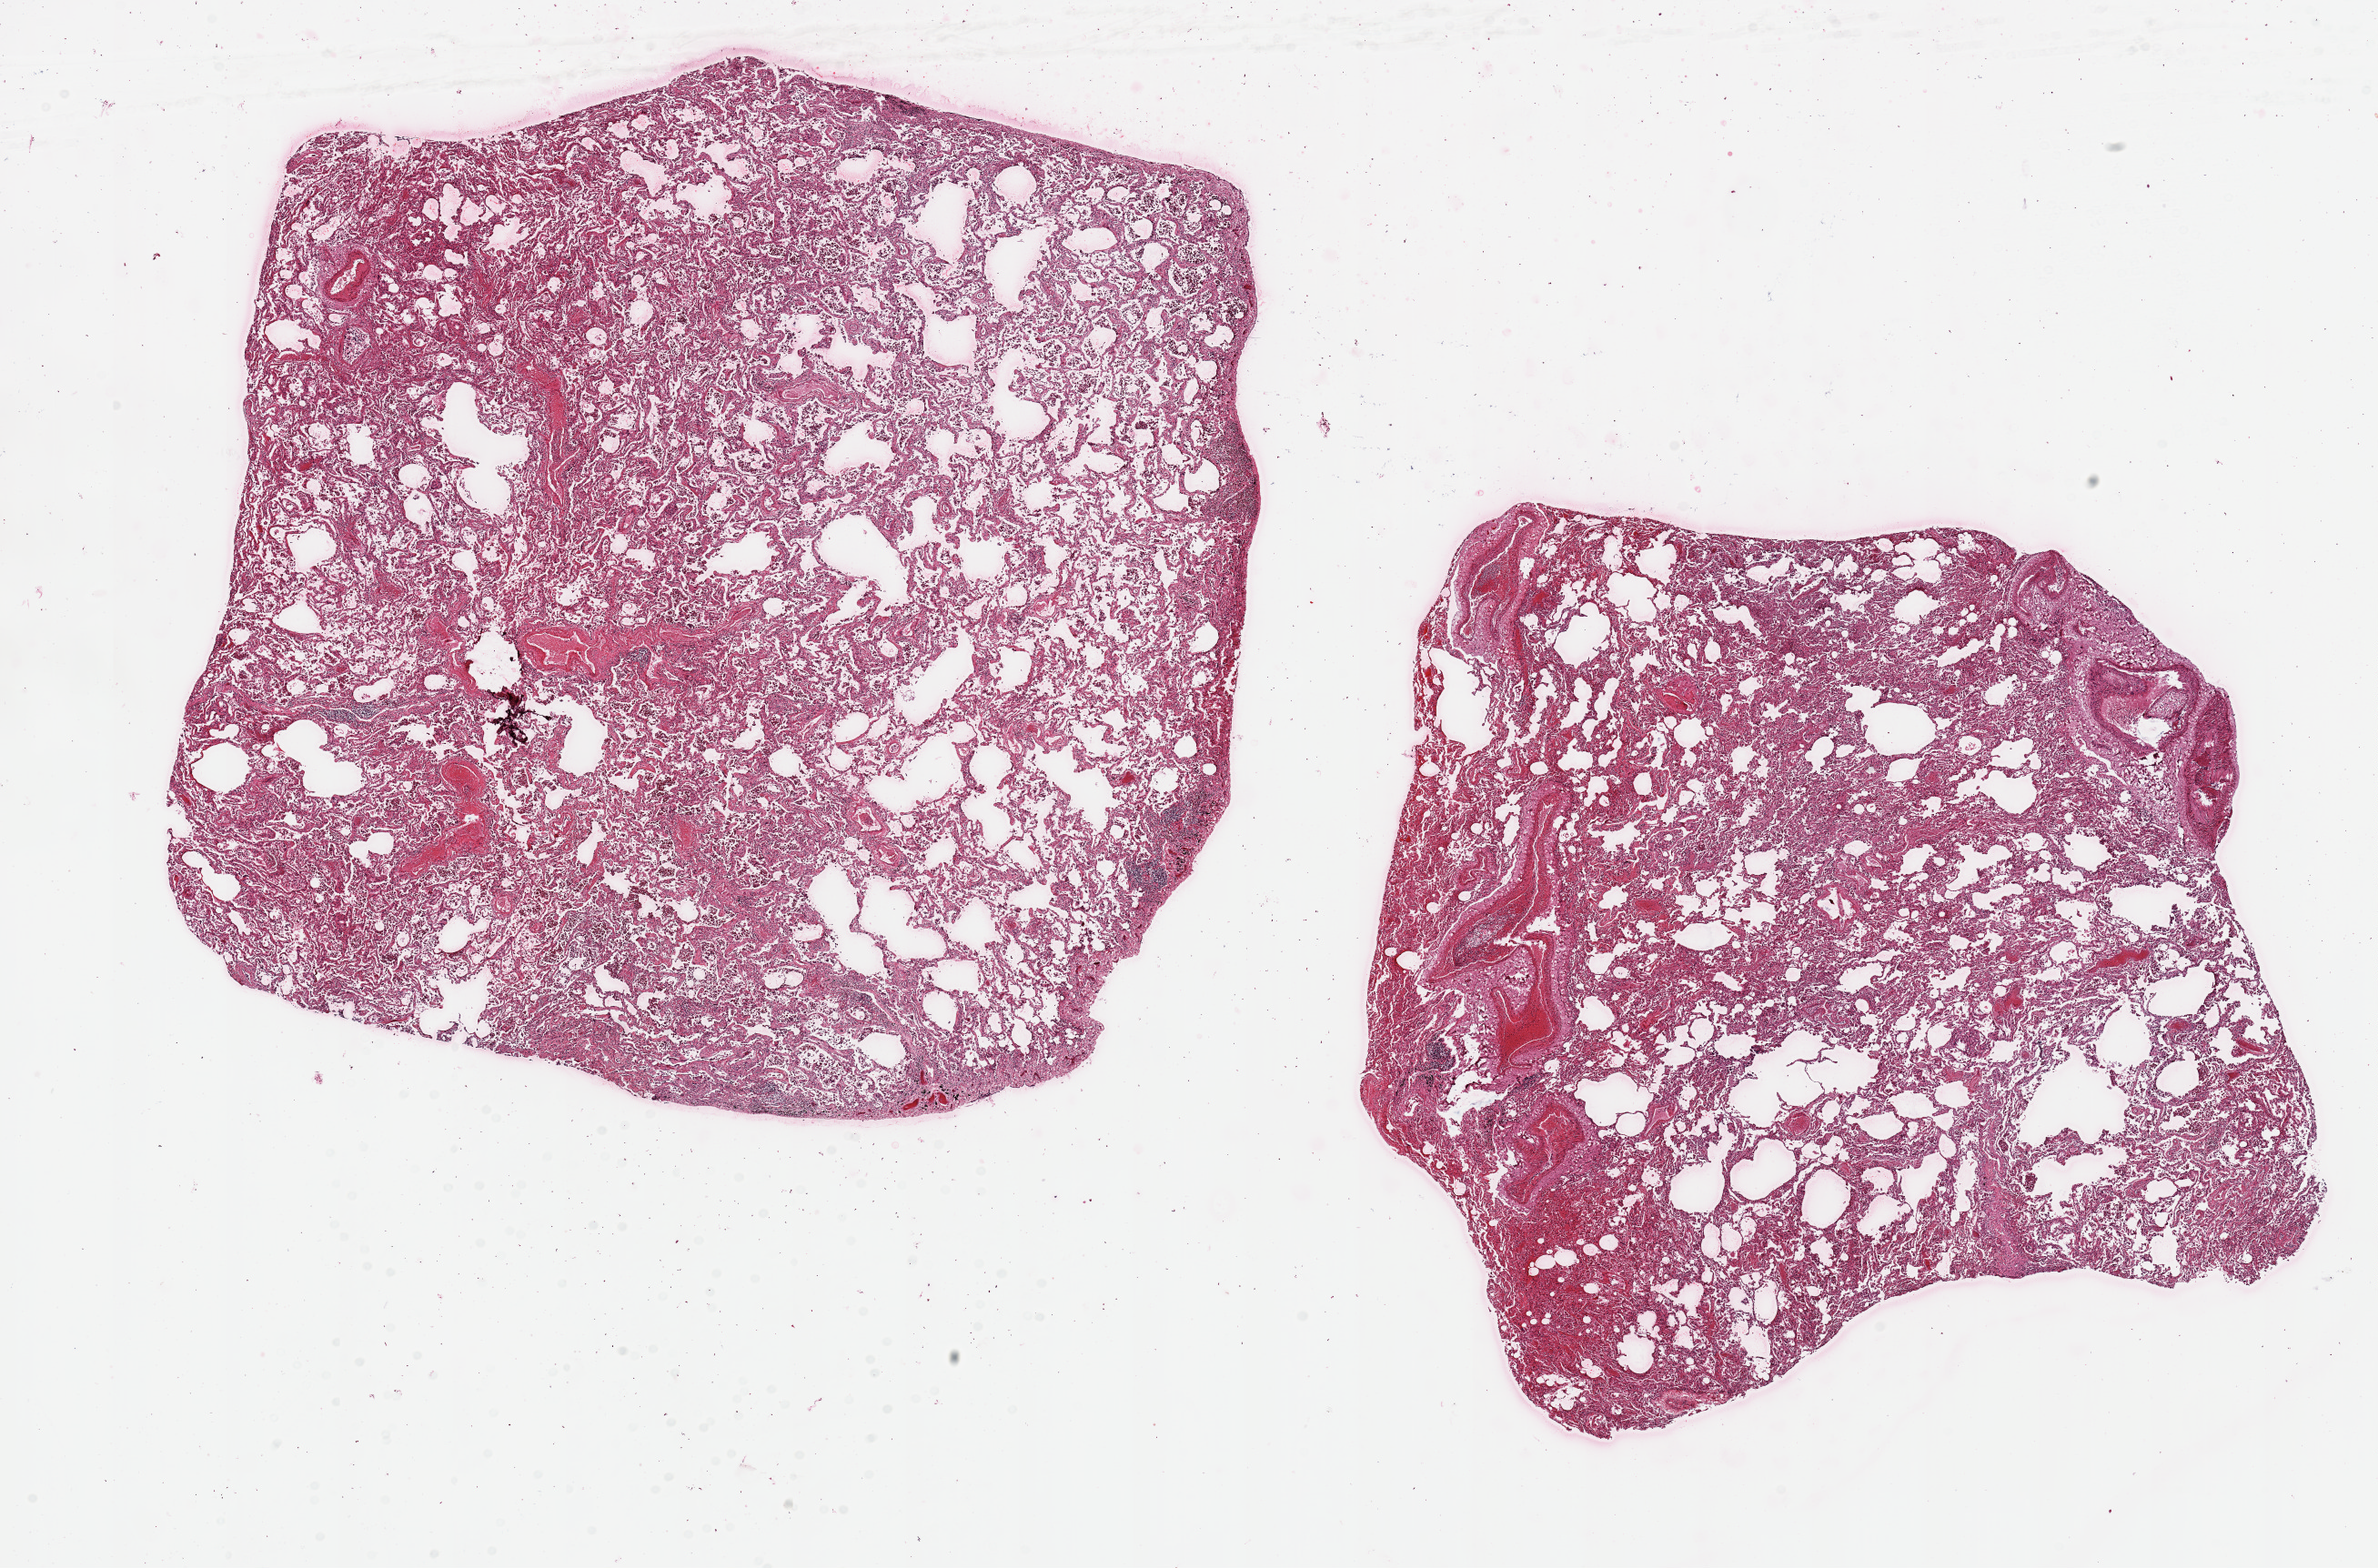
Digitized hematoxylin and eosin (H&E)-stained section, brightfield, low-resolution overview of the scanned area, about 20.7 x 13.6 mm; PAXgene-fixed paraffin-embedded (PFPE) section; target tissue: lung; donor tissue sample. Donor: male.
Review note (as recorded): 2 pieces, 9x9 & 8x8 mm; patchy emphysema & interstitial fibrosis.